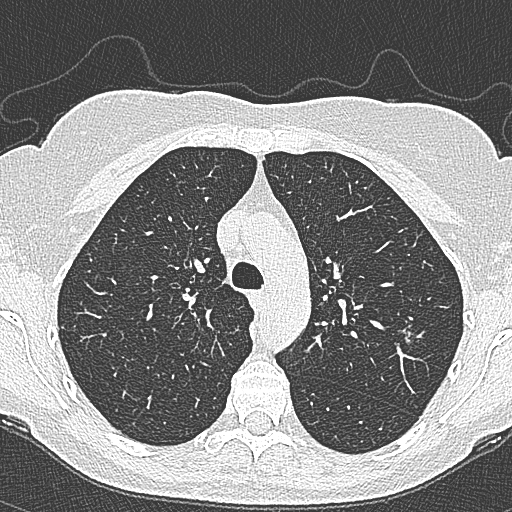
Axial slice from a low-dose chest CT screening exam. Second screening round (one year after baseline). Lung window (W 1500 / L -600 HU). Slice 92 of 350 in the series. Female participant, aged 65 years at enrolment.
- Expert reader's lesion annotation, bounding box (x1, y1, x2, y2) in pixels: (390, 308, 435, 353).
- The screening reader recorded 4 non-calcified nodules or masses ≥4 mm on this exam (left upper lobe, left upper lobe, left upper lobe, right lower lobe); which of them this box marks is not recorded.
- Lung cancer was diagnosed 54 days after this screen: bronchiolo-alveolar carcinoma, non-mucinous, left upper lobe, stage IA (AJCC 6th edition), 10 mm at pathology.